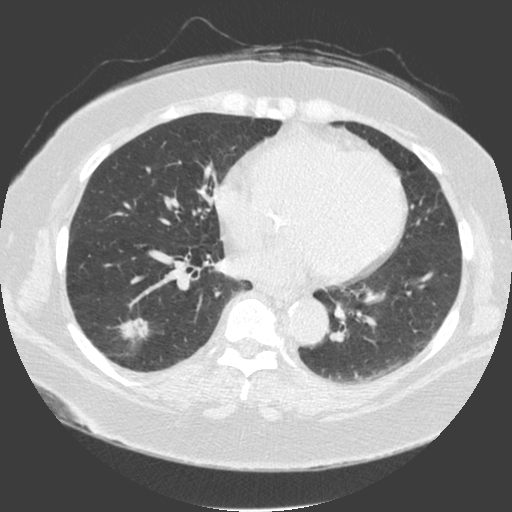
Chest CT (low-dose screening protocol), one axial image. Third annual screen. Lung window (W 1500 / L -600 HU). Standard (soft-tissue) reconstruction kernel (C). 120 kVp. 512 × 512 image matrix. Female participant, aged 56 years at enrolment. Current smoker at enrolment.
Expert-annotated lung lesion, bounding box (x1, y1, x2, y2) in pixels: (109, 305, 159, 351). The screening reader recorded 4 non-calcified nodules or masses ≥4 mm on this exam (left lower lobe, right lower lobe, right lower lobe, right lower lobe); which of them this box marks is not recorded. Official screen result: positive, other. Later outcome: lung cancer diagnosed 20 days after this screen — adenosquamous carcinoma, right lower lobe, poorly differentiated (G3), stage IA (AJCC 6th edition), 25 mm at pathology.